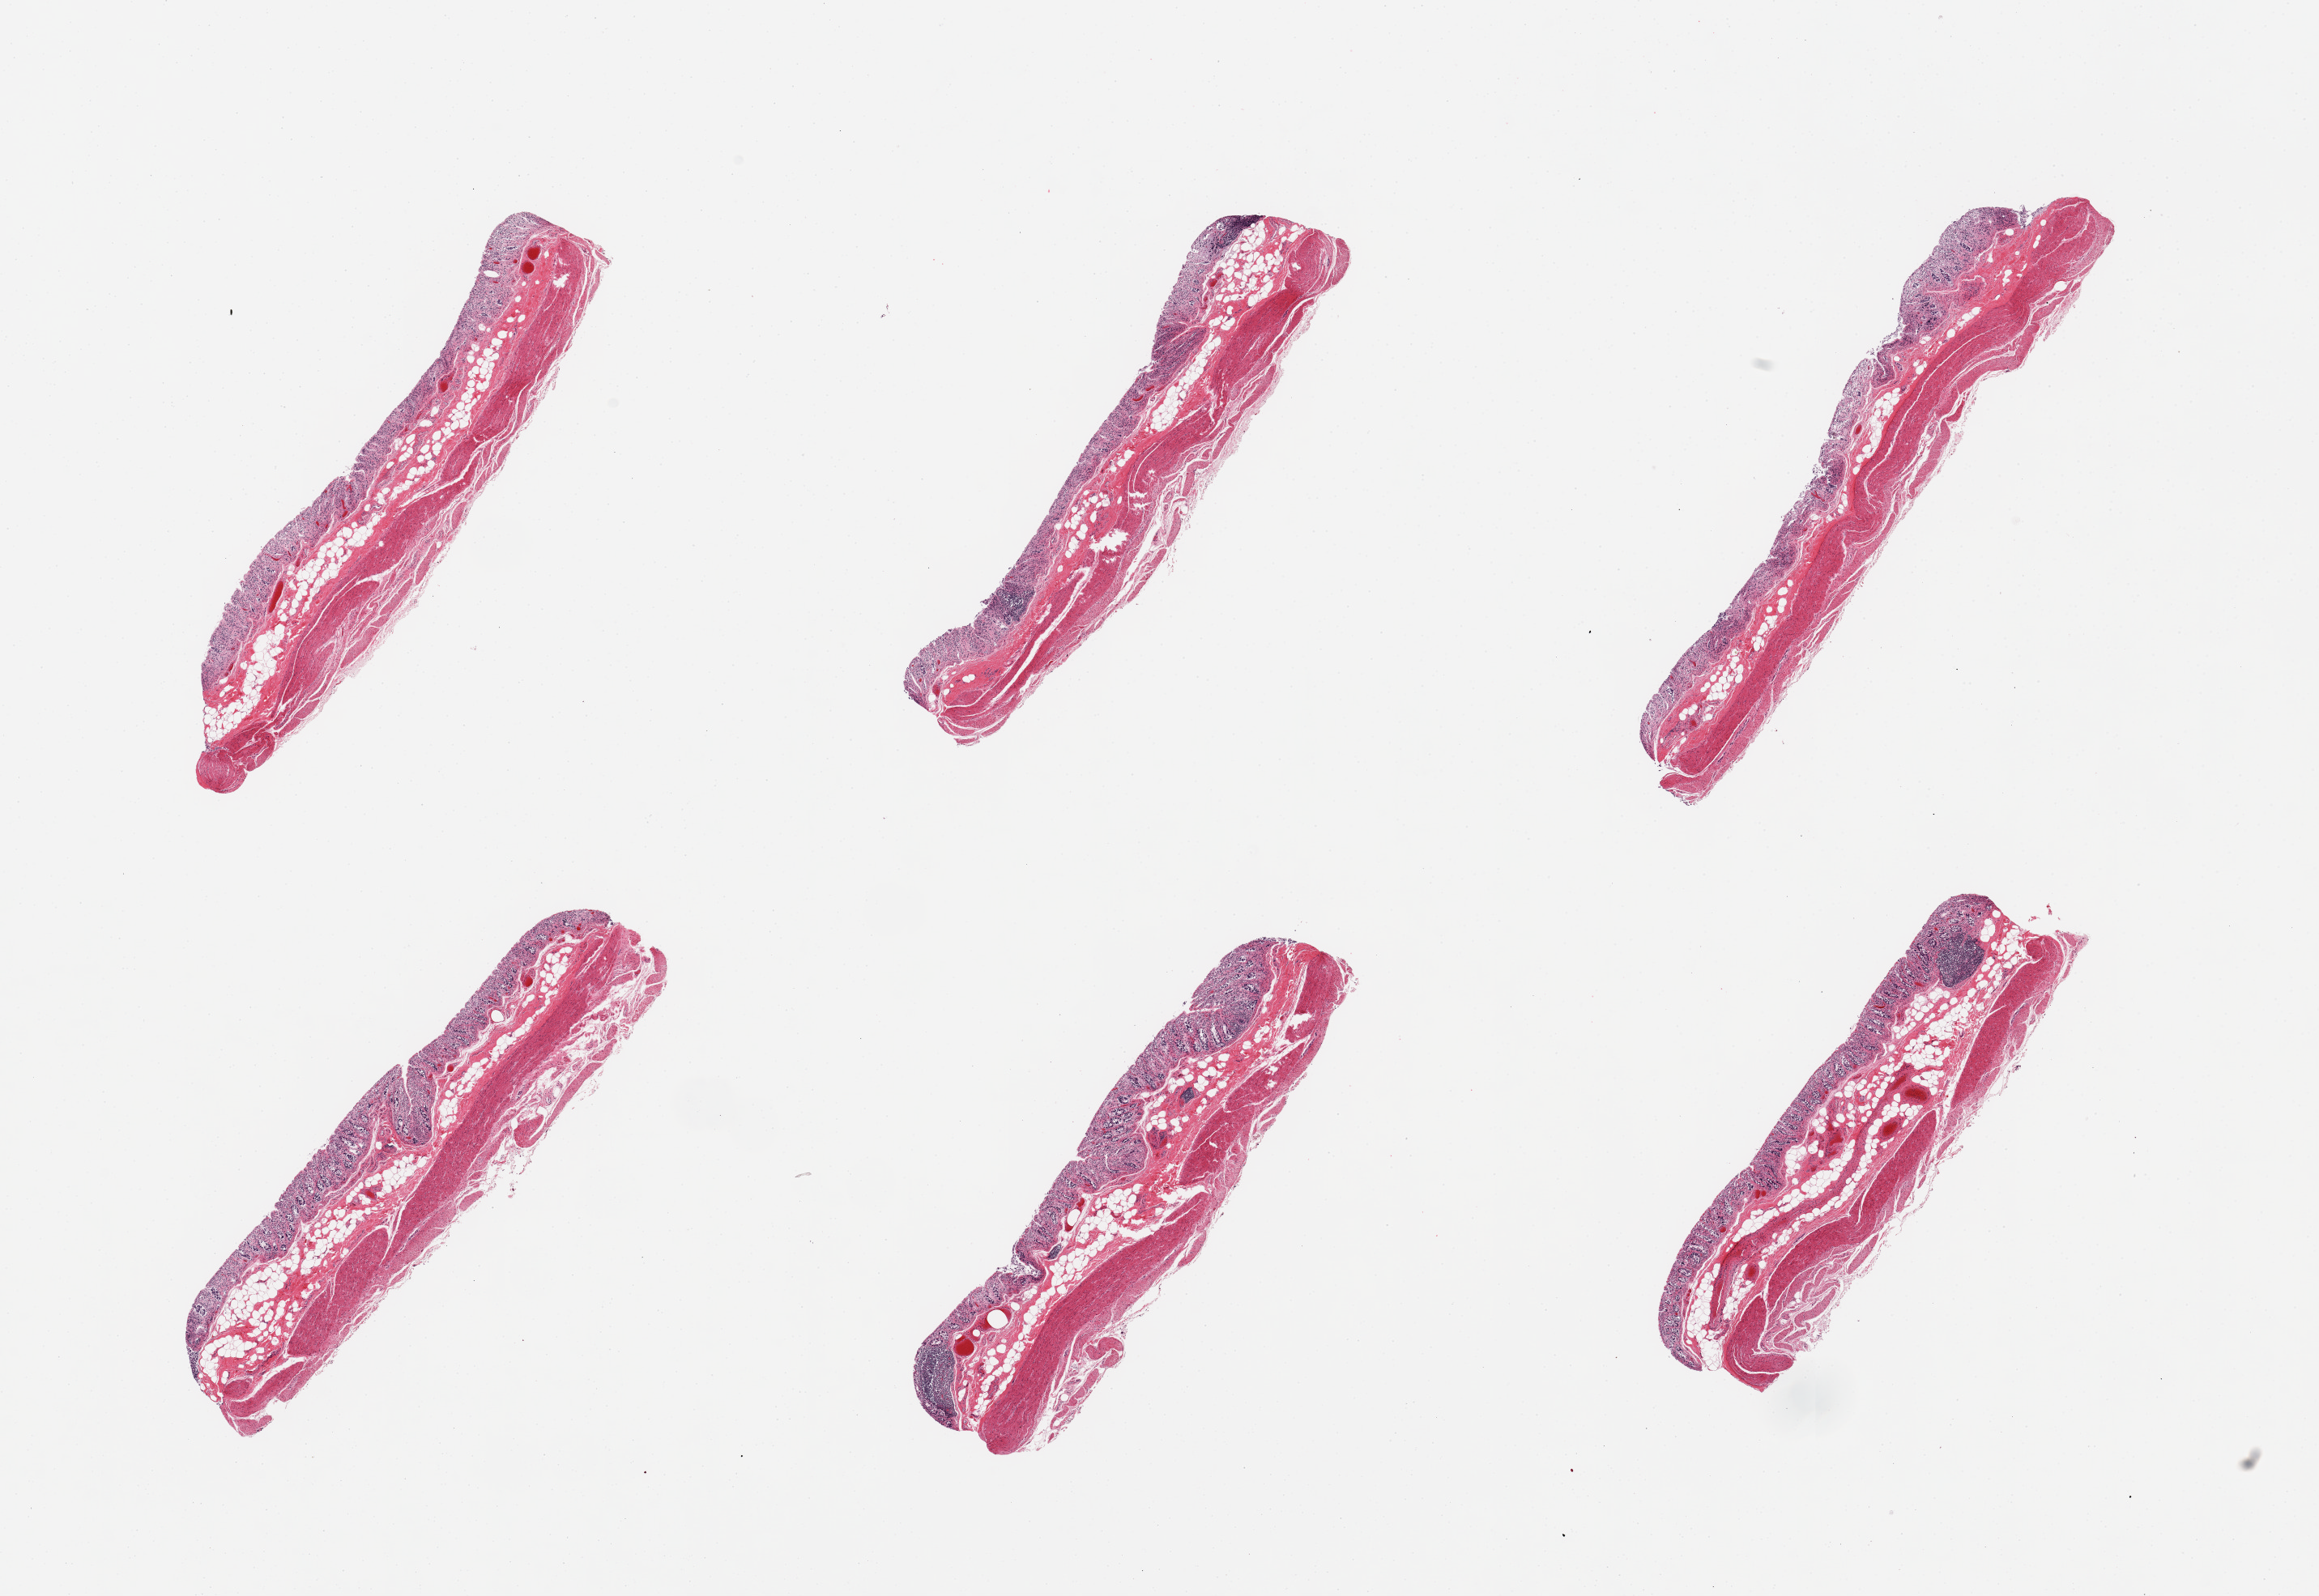
H&E whole-slide image — low-resolution overview of the scanned area, about 22.6 x 15.6 mm; PAXgene-fixed paraffin-embedded (PFPE) section; sampled site (target tissue): transverse colon; donor tissue sample. Donor sex: male.
- reviewer comment on this tissue sample: 6 pieces; mucosa mostly autolyzed